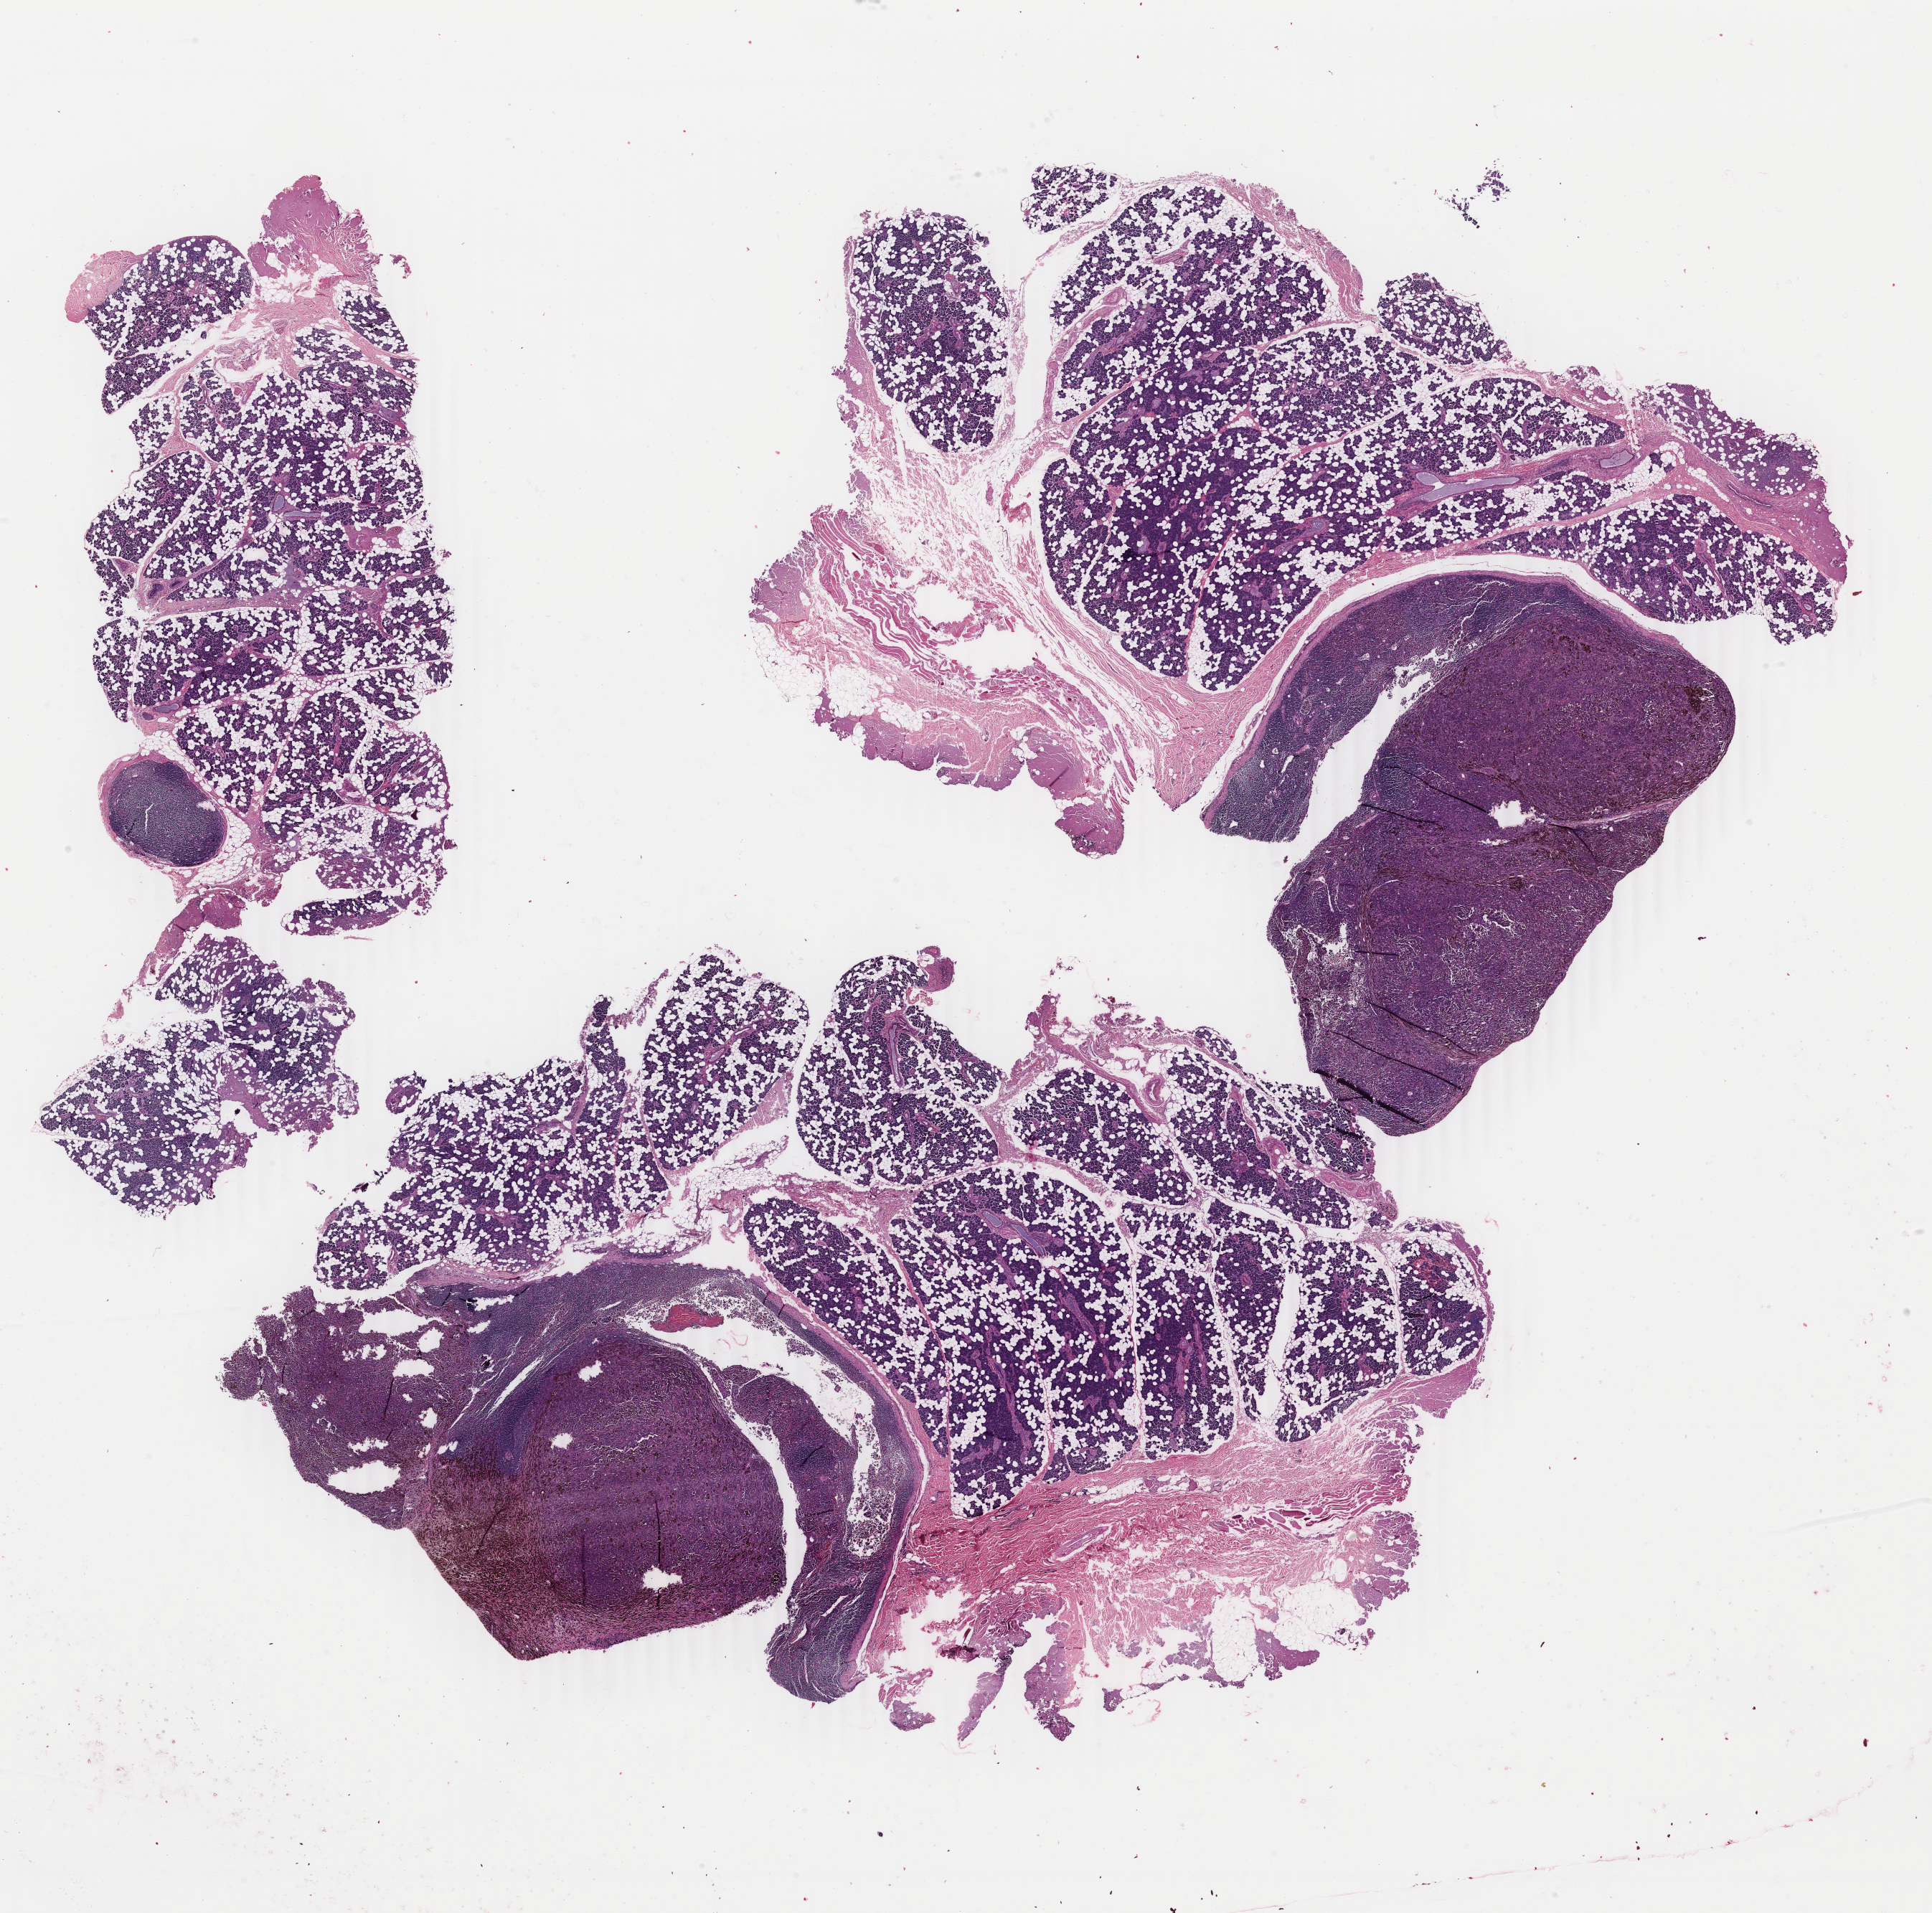
H&E whole-slide image, whole scanned area (about 21.4 x 21.2 mm, from a 40x scan) shown as a low-resolution overview, FFPE section, skin, primary tumour sample. Female patient; age at initial diagnosis 58 years.
Pathologic diagnosis: Malignant melanoma, NOS.